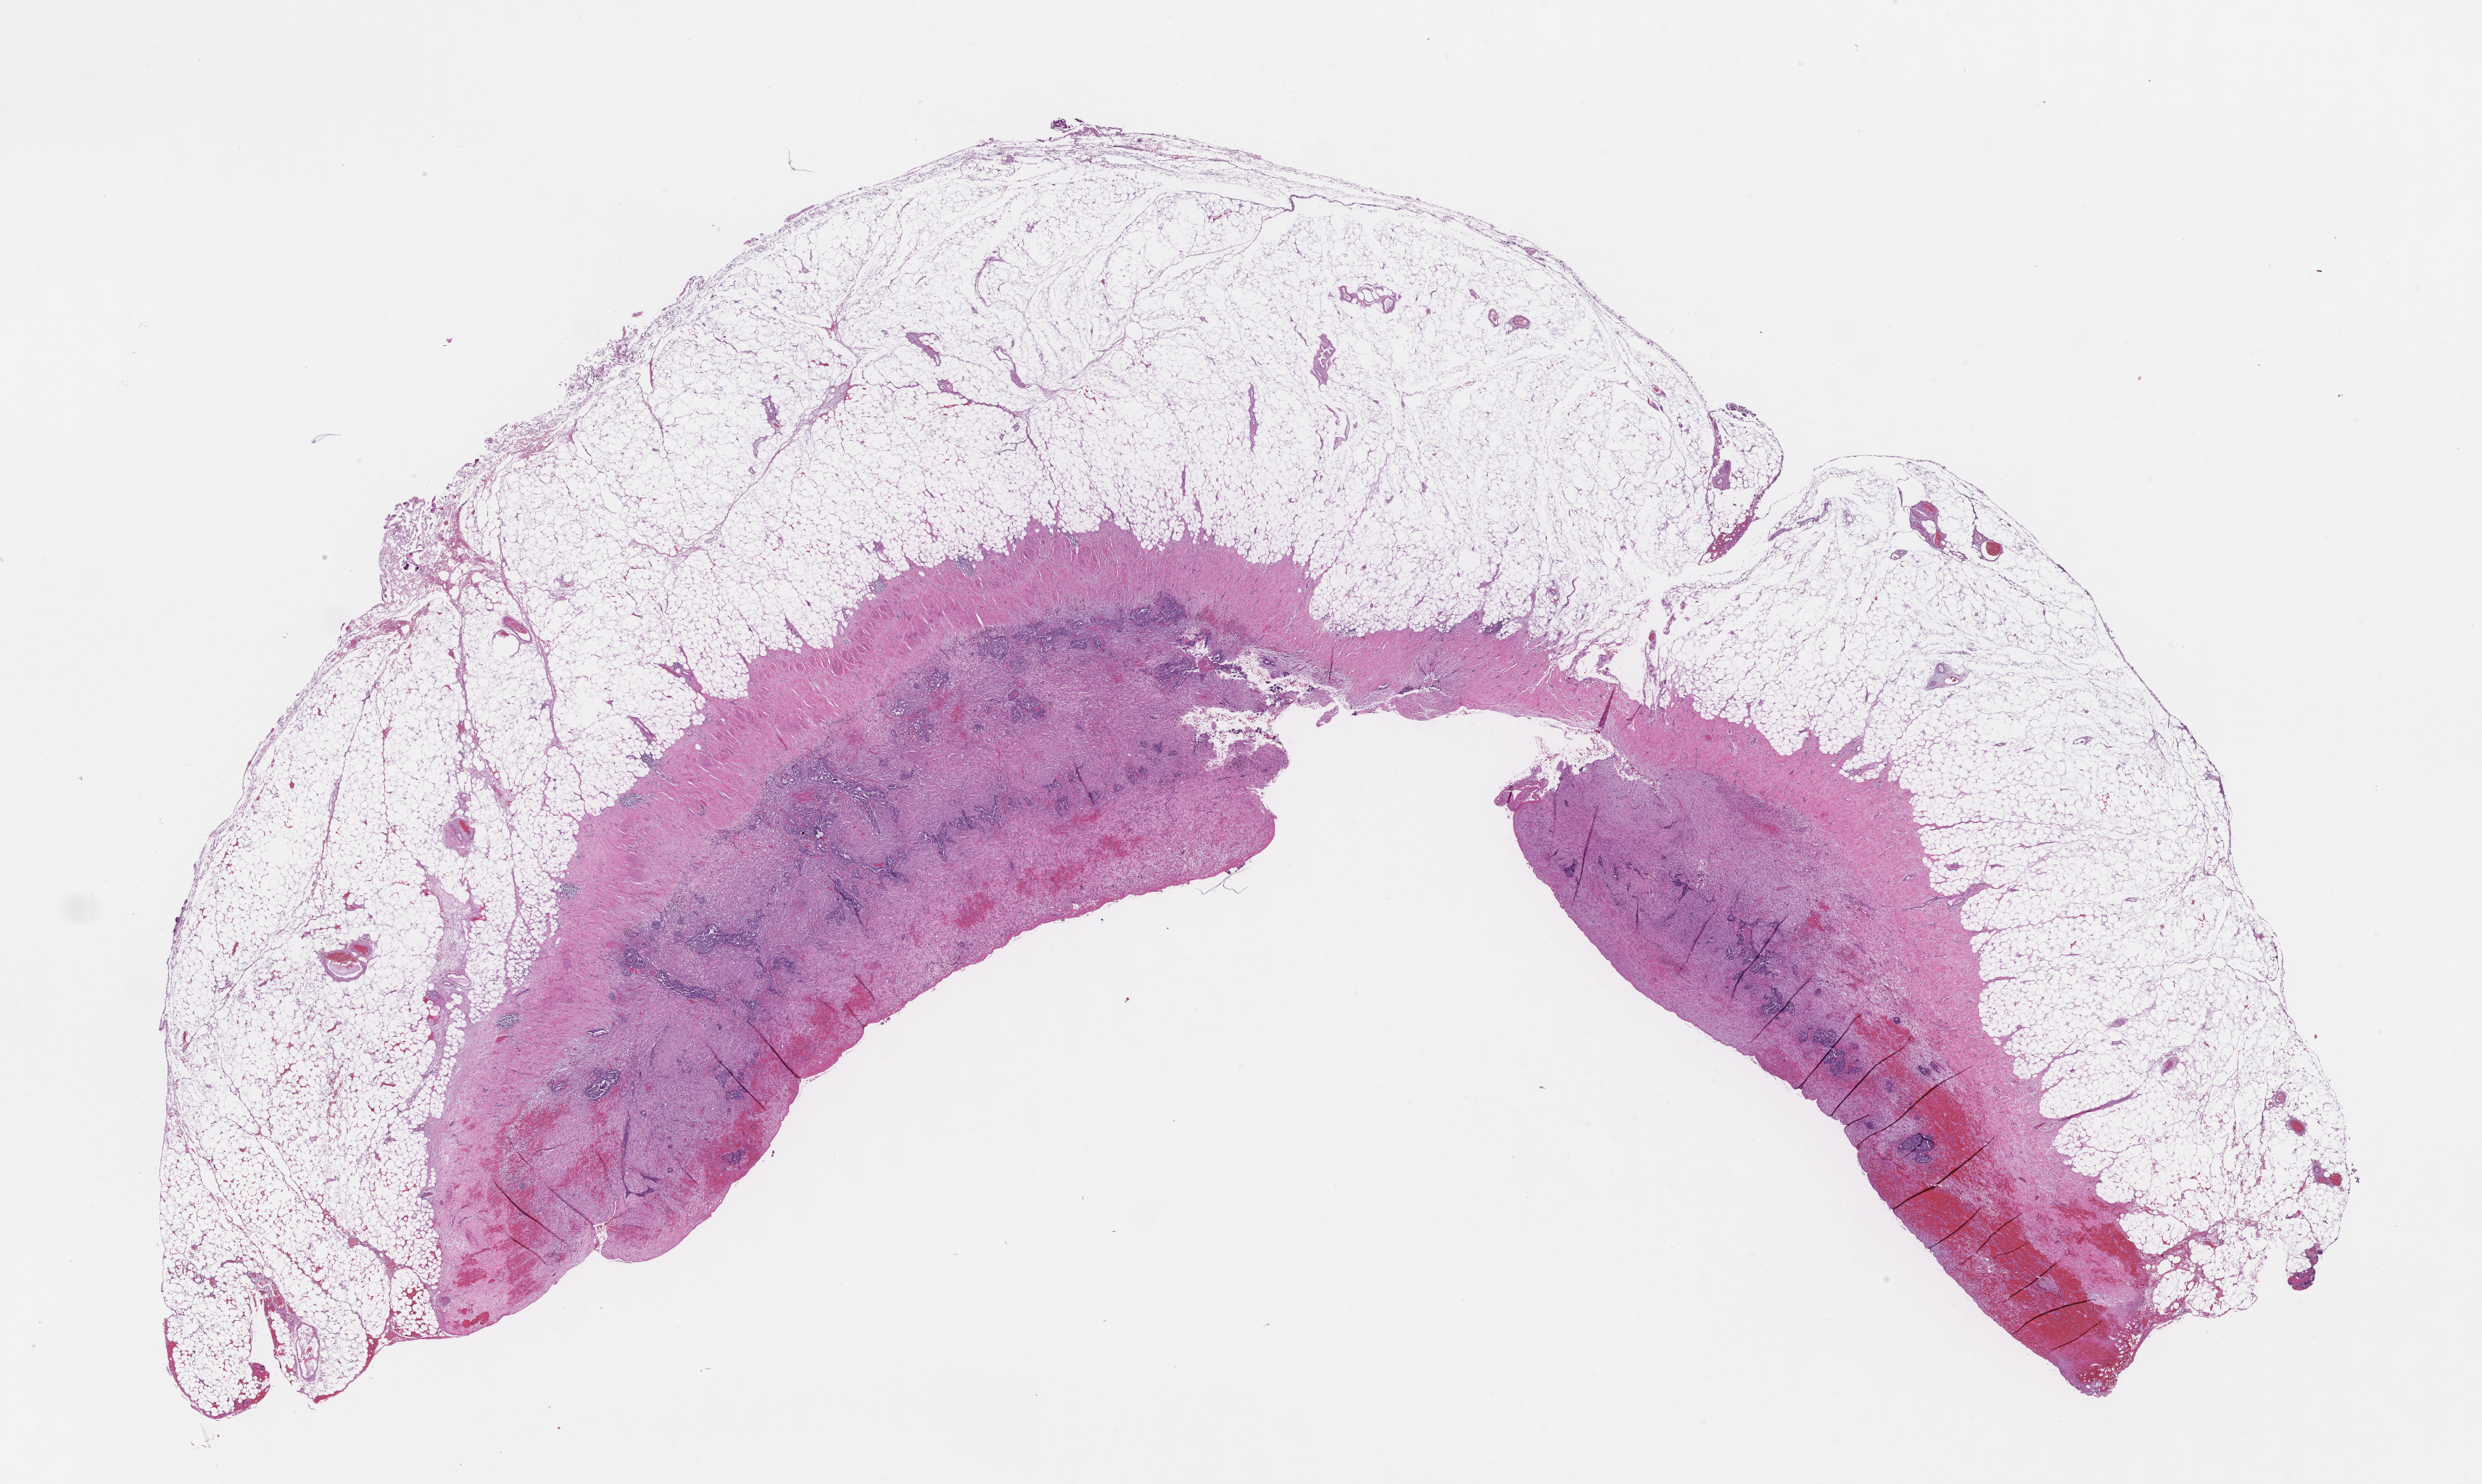
Whole-slide image, H&E stain — shown as a low-resolution overview of the whole scanned area (about 27.6 x 16.5 mm); formalin-fixed paraffin-embedded section; site: ovary. Female patient.
This section: primary tumour tissue. Diagnosis: Fallopian Tube Carcinoma.